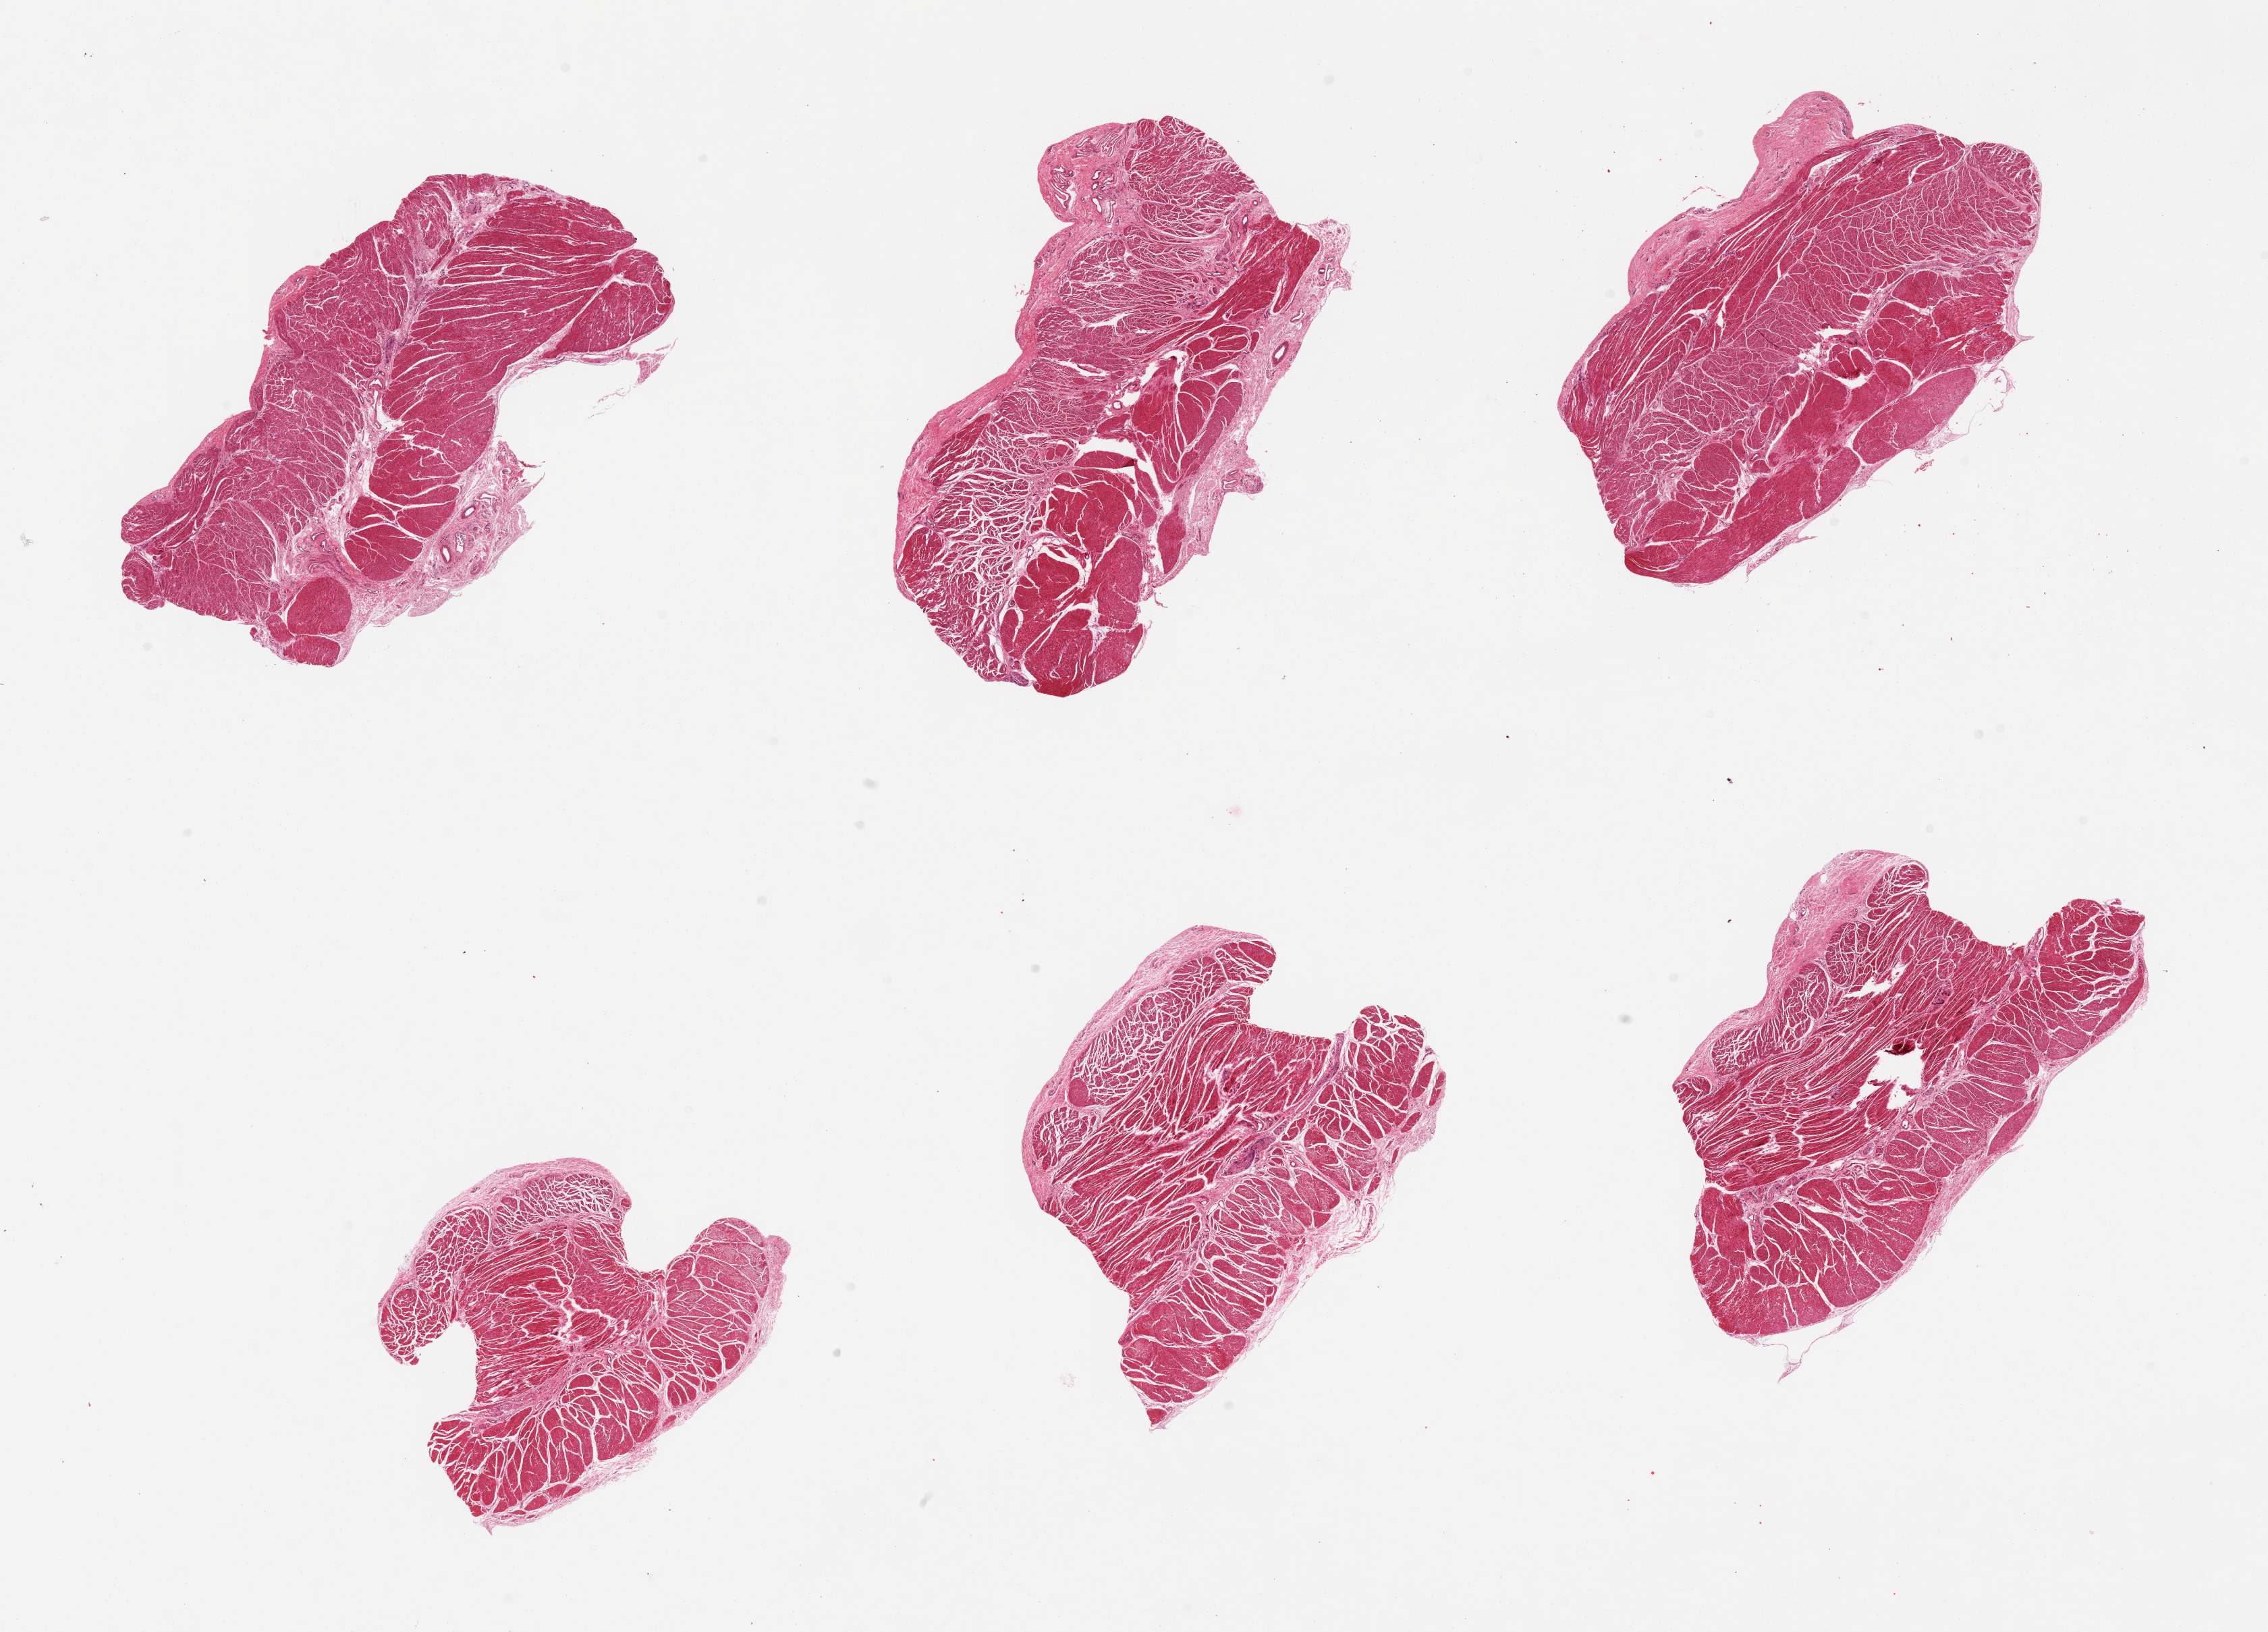
H&E whole-slide image — low-resolution overview of the scanned area, about 26.6 x 19.1 mm, PAXgene-fixed, paraffin-embedded tissue, target tissue: esophageal muscle, donor tissue sample. Male donor.
• review note (as recorded): 6 pieces; well dissected